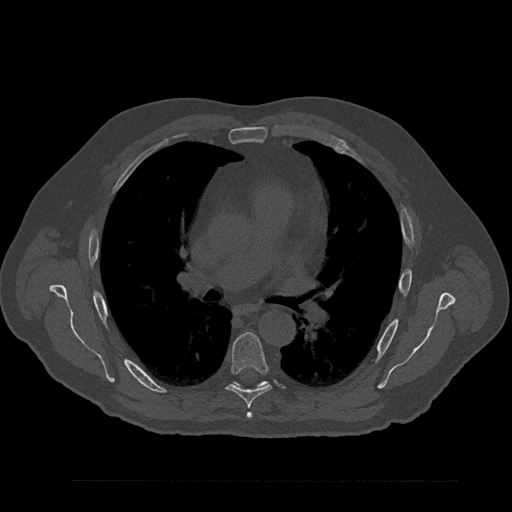
CT including the spine, one axial slice; slice 549 of 797 in the series (ordered by position); reconstruction kernel Br40s/3; 120 kVp; bone window (W 1800 / L 400 HU); 512 × 512 image matrix, field of view 430 × 430 mm. Patient: male, 61 years. Case-level facts recorded for this patient, not image findings: primary cancer: prostate.
Annotated regions visible in this slice (semi-automatic segmentation, software-assisted and operator-edited):
- T5 vertebra: box from (x=247, y=413) to (x=252, y=418) px
- T6 vertebra: (x=226, y=332)–(x=272, y=415)
- T7 vertebra: (x=235, y=381)–(x=268, y=387)